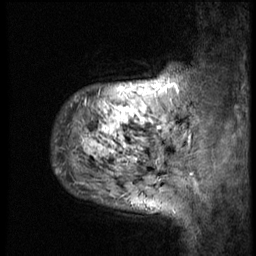
Breast MRI (dynamic contrast-enhanced), one sagittal slice; position 7 of 58 along the scan axis; 3 images stored at this slice position (order not interpretable as contrast timing); 1.5 T; TE 4.2 ms, TR 9 ms; 256 × 256 image matrix, field of view 180 × 180 mm. Patient: female, 50 years. Case-level facts recorded for this patient, not image findings: setting: breast cancer imaged before/during neoadjuvant chemotherapy; receptor status: triple-negative.
Structures marked on this image (semi-automatic segmentation, software-assisted and operator-edited):
- analysis volume of interest (the breast-tissue region the enhancement analysis was run in; not a lesion): bounding box (x1, y1, x2, y2) in pixels: (53, 55, 186, 214)
- tumour enhancement mask (voxels above the 140 % enhancement threshold inside the analysis volume of interest): (58, 88, 167, 172)